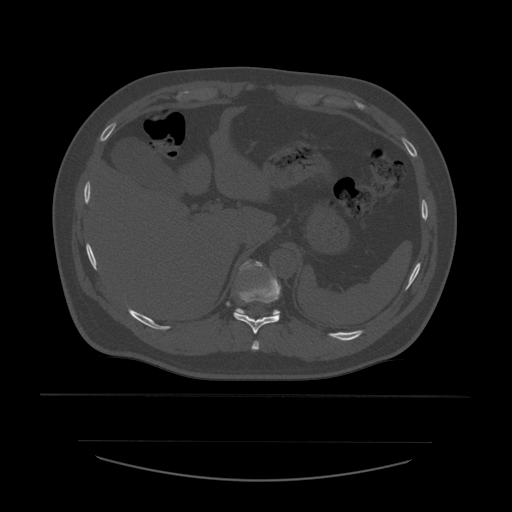
CT including the spine, one axial slice; position 291 of 532 along the scan axis; reconstruction kernel STANDARD; bone window (W 1800 / L 400 HU); 1.25 mm slice thickness; 512 × 512 image matrix. Patient age 44 years. Case-level facts recorded for this patient, not image findings: primary cancer: soft tissue sarcoma.
Outlined on this slice (semi-automatic segmentation, software-assisted and operator-edited):
- T10 vertebra: bounding box <234,262,281,334> (left, top, right, bottom; pixels)
- T11 vertebra: <236,260,281,315>
- T9 vertebra: <252,341,260,350>